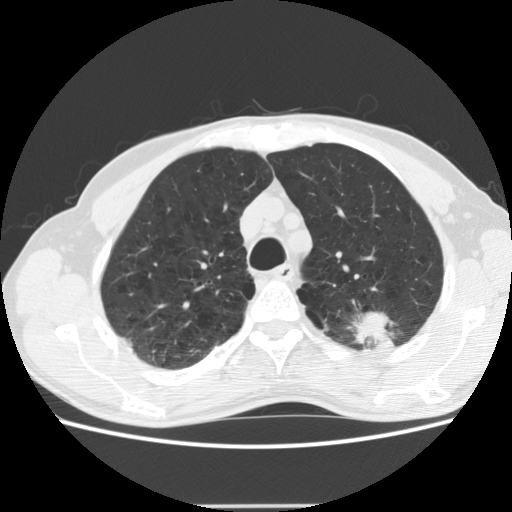
Axial slice from a low-dose chest CT screening exam; baseline annual screen; lung window (W 1500 / L -600 HU); slice 42 of 191 in the series. Male, age 64 years at enrolment. Current smoker at enrolment.
- Expert reader's lesion annotation, box from (x=340, y=287) to (x=429, y=358) px.
- Screening reader's record for this exam (one nodule recorded; not confirmed to be the boxed lesion): non-calcified nodule or mass ≥4 mm, left upper lobe, 27 × 19 mm, poorly defined margins, soft tissue attenuation.
- Participant outcome: lung cancer diagnosed 23 days after this screen — adenocarcinoma, NOS, left upper lobe, moderately differentiated (G2), stage IA (AJCC 6th edition), 29 mm at pathology.